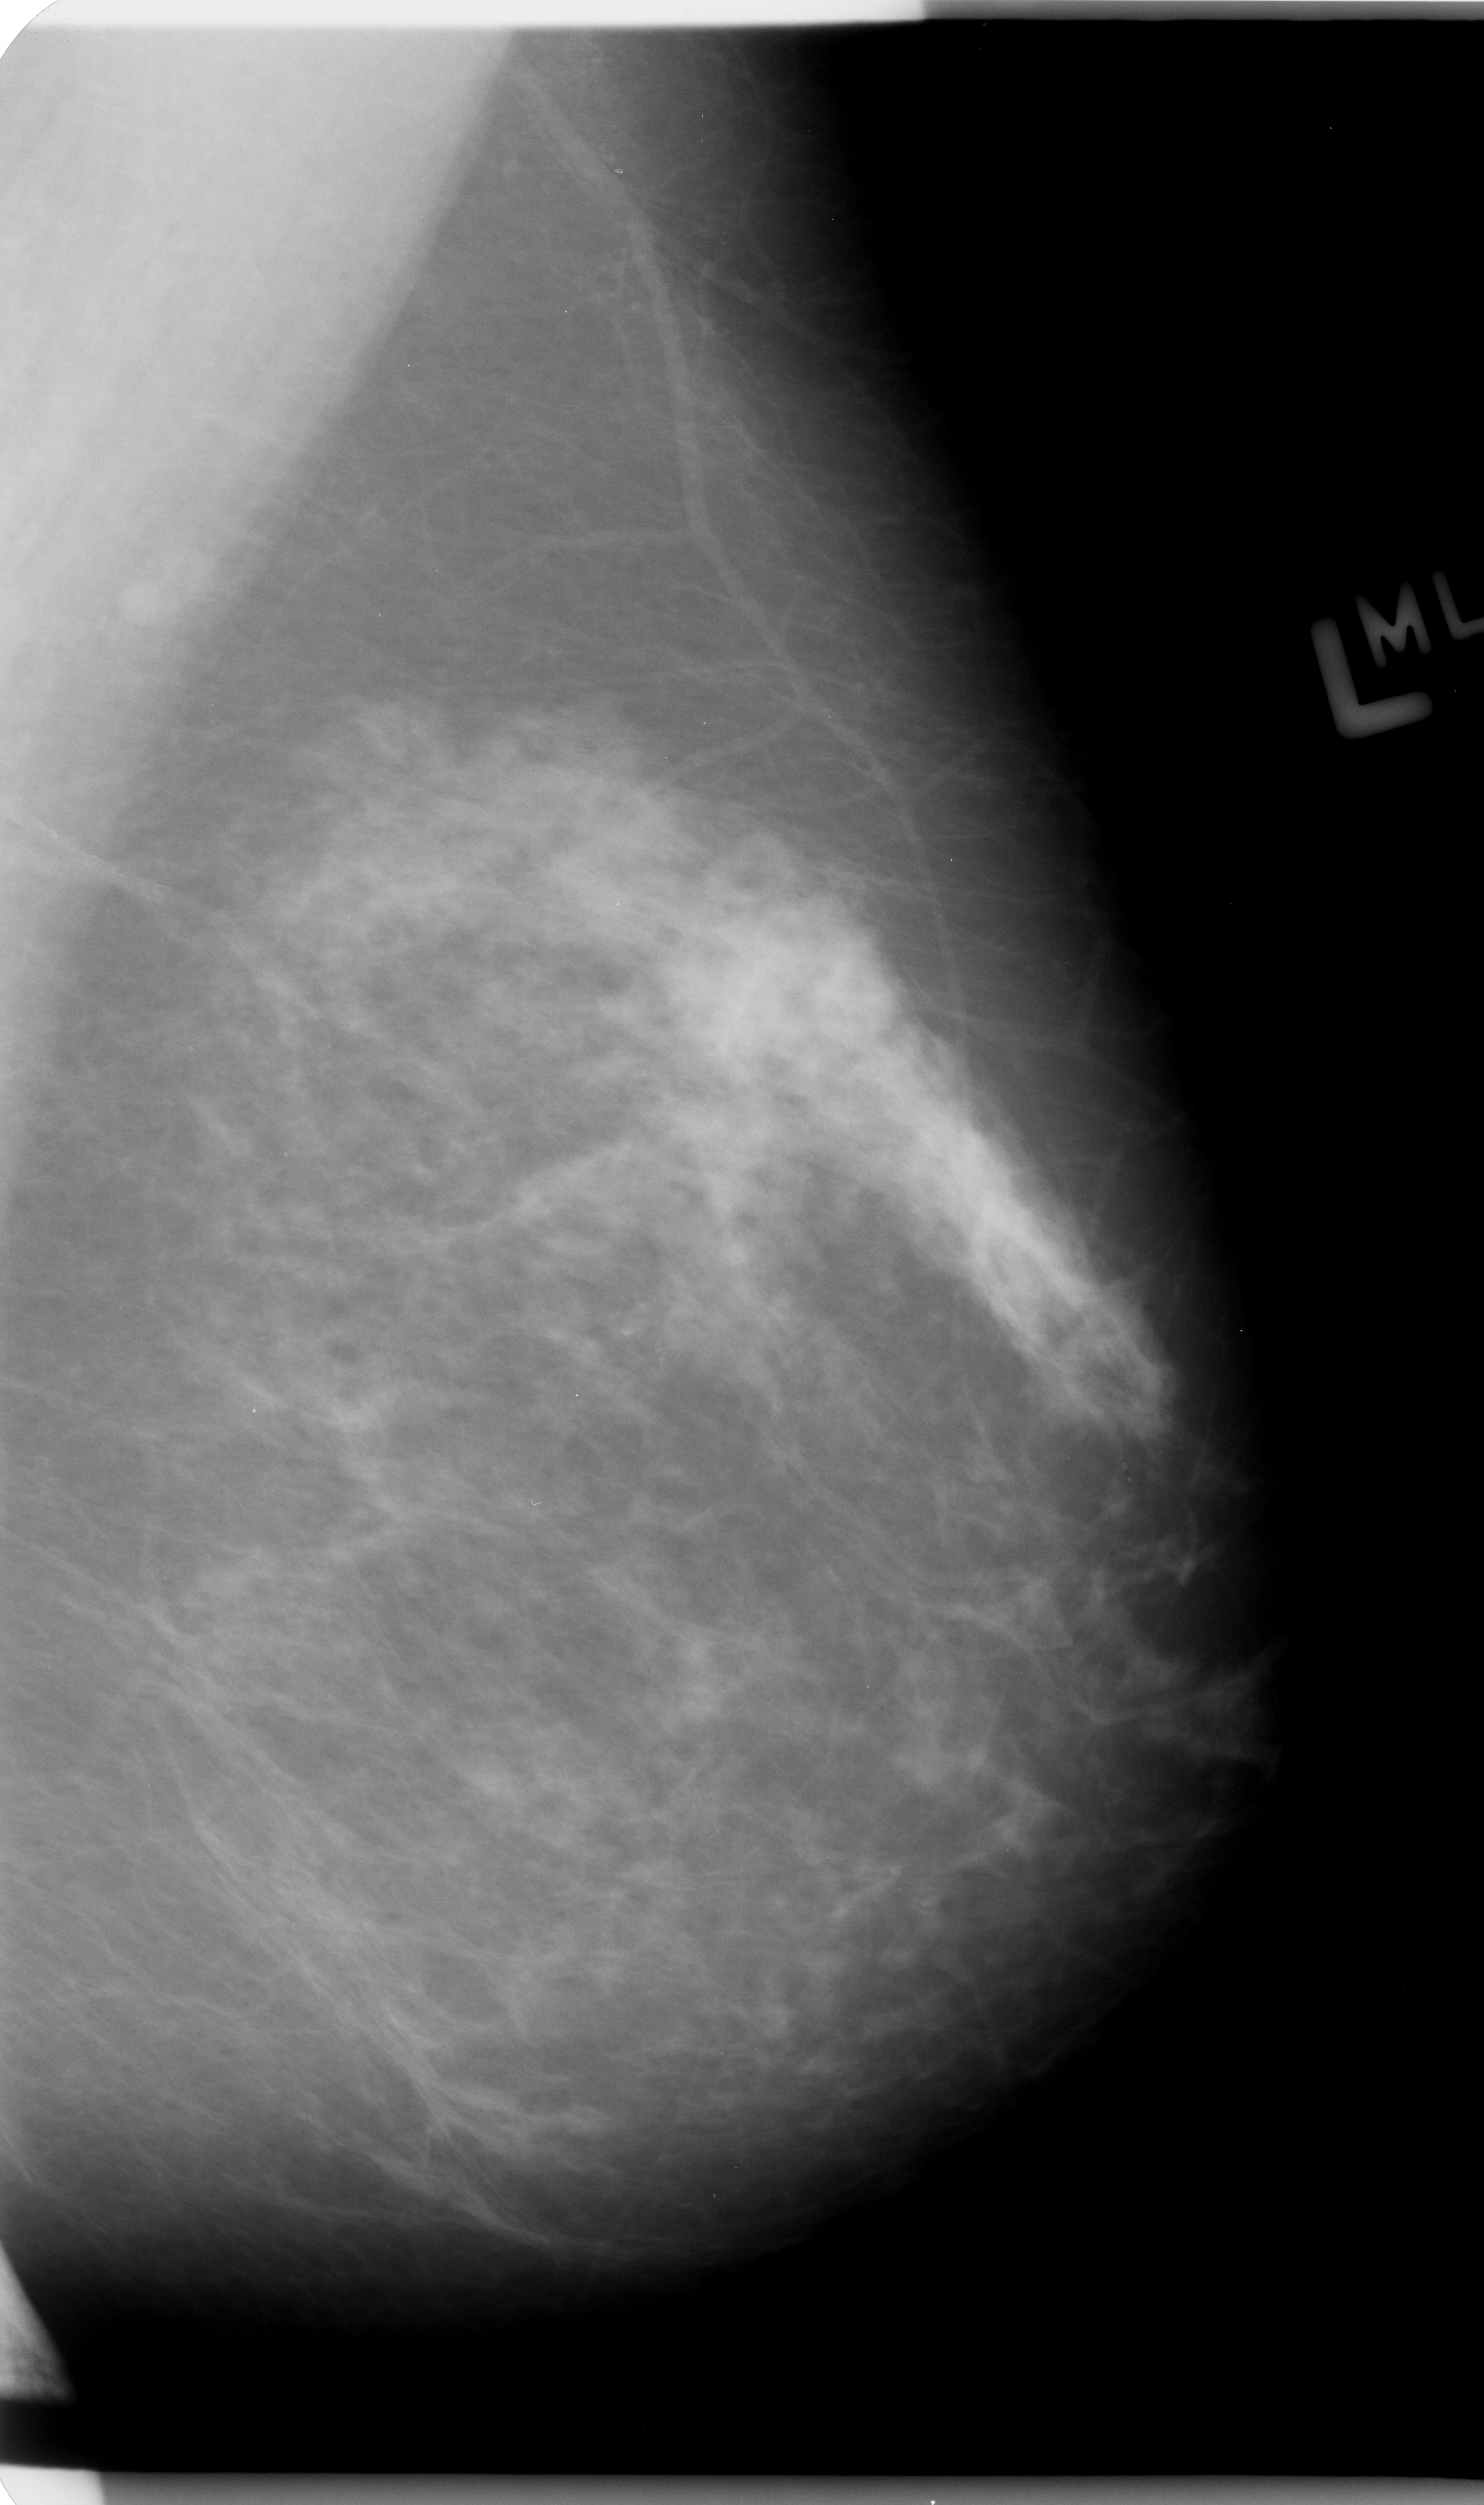
Scanned film-screen mammogram. Left breast. Mediolateral oblique (MLO) view. BI-RADS breast density category 2 (scale 1–4). 1484 × 2505 image matrix.
Expert-marked regions of interest on this image (one box per marked abnormality):
- calcifications, morphology pleomorphic, distribution clustered; BI-RADS assessment category 4; pathology result (as recorded, not read from the image): benign: box from (x=518, y=1218) to (x=722, y=1485) px